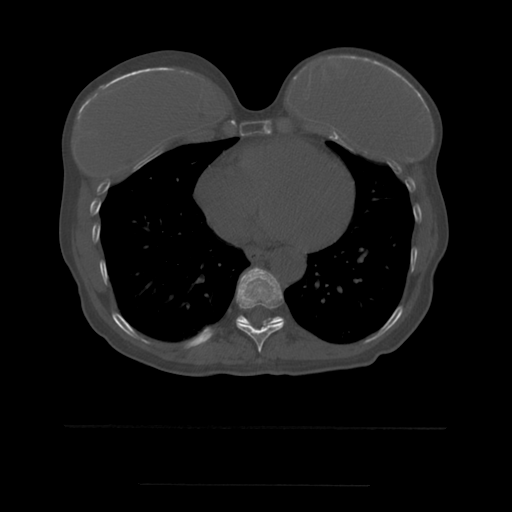
CT including the spine, one axial slice; bone window (W 1800 / L 400 HU); 512 × 512 image matrix, field of view 350 × 350 mm. Patient age 58 years. From the clinical record (not read from this slice): primary cancer: lung.
Outlined on this slice (semi-automatically segmented with operator editing):
- T10 vertebra: bounding box [x1, y1, x2, y2] px = [237, 316, 283, 327]
- T9 vertebra: [236, 267, 284, 353]